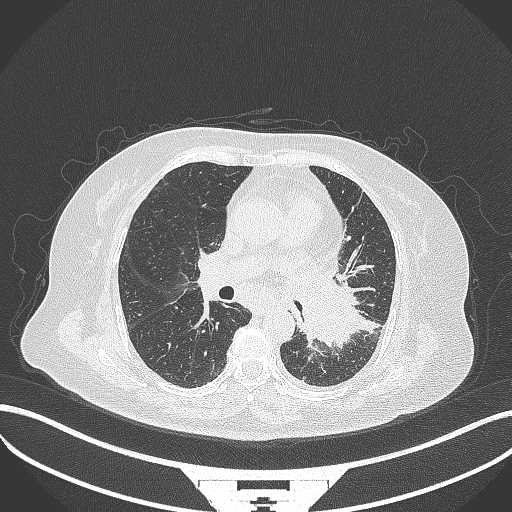
Chest CT, one axial slice. Reconstruction kernel B70f. 120 kVp. Lung window (W 1500 / L -600 HU). 1 mm slice thickness. 512 × 512 image matrix, field of view 400 × 400 mm. Patient: female, 69 years. Case-level facts recorded for this patient, not image findings: clinical TNM (as recorded): T2b N3 M1.
Structures marked on this image (bounding box drawn by a radiologist):
- lung tumour (recorded histology: adenocarcinoma): bounding box <300,278,366,350> (left, top, right, bottom; pixels)